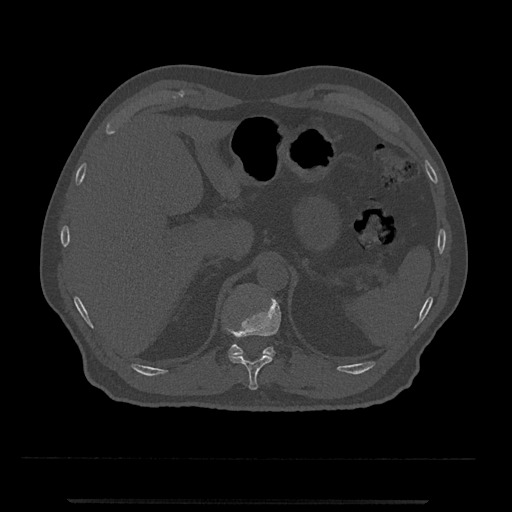
CT including the spine, one axial slice; slice 441 of 797 in the series (ordered by position); 120 kVp; bone window (W 1800 / L 400 HU); 512 × 512 image matrix, field of view 419 × 419 mm. Male patient, age 63 years. Case-level facts recorded for this patient, not image findings: primary cancer: prostate.
Outlined on this slice (semi-automatic segmentation, software-assisted and operator-edited):
- T11 vertebra: bounding box <228,298,281,390> (left, top, right, bottom; pixels)
- T12 vertebra: <228,344,275,357>